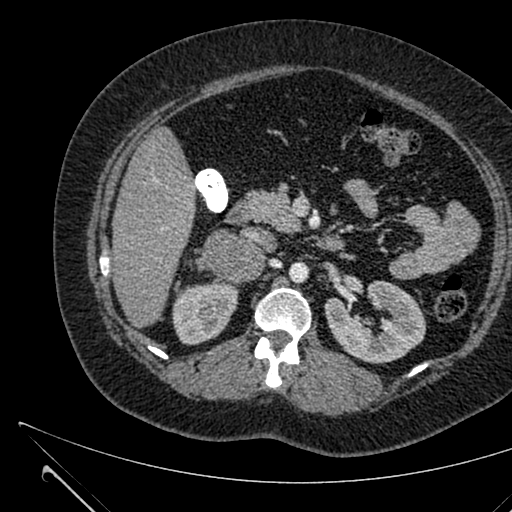
Contrast-enhanced abdominal CT, one axial slice; slice 363 of 731 in the series (ordered by position); 120 kVp; intravenous contrast given; soft-tissue window (W 400 / L 40 HU); 1 mm slice thickness; 512 × 512 image matrix, field of view 376 × 376 mm. Female patient, age 36 years. Case-level facts recorded for this patient, not image findings: diagnosis: adrenocortical carcinoma; tumour side: right adrenal; tumour size at pathology: 10 cm; Ki-67 index: 20 %; stage (as recorded): 4.
Outlined on this slice (semi-automatic segmentation, software-assisted and operator-edited):
- mass: bounding box (x1, y1, x2, y2) in pixels: (201, 229, 264, 283)